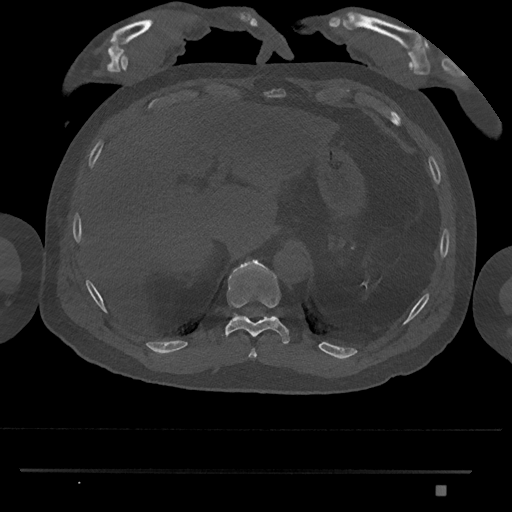
CT including the spine, one axial slice; position 997 of 1134 along the scan axis; reconstruction kernel Br40s/3; bone window (W 1800 / L 400 HU); 0.5 mm slice thickness; 512 × 512 image matrix, field of view 429 × 429 mm. Patient: male, 65 years. From the clinical record (not read from this slice): primary cancer: prostate.
Outlined on this slice (semi-automatically segmented with operator editing):
- T10 vertebra: box from (x=225, y=259) to (x=290, y=345) px
- T11 vertebra: (x=234, y=313)–(x=245, y=318)
- T9 vertebra: (x=248, y=348)–(x=257, y=360)